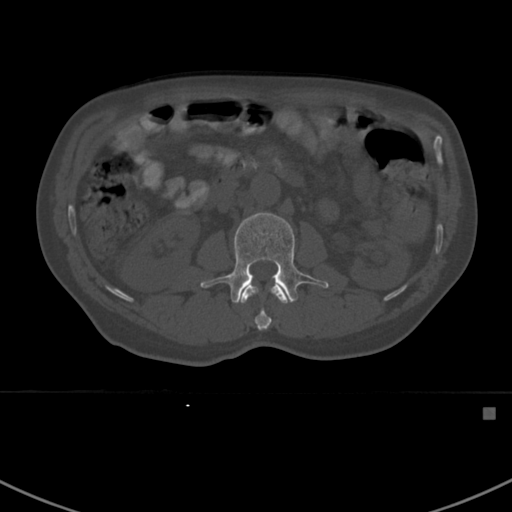
CT including the spine, one axial slice; slice 292 of 412 in the series (ordered by position); reconstruction kernel Br40s; 120 kVp; bone window (W 1800 / L 400 HU); 1.5 mm slice thickness; 512 × 512 image matrix. Patient: male, 59 years. From the clinical record (not read from this slice): primary cancer: prostate.
Structures marked on this image (semi-automatically segmented with operator editing):
- L1 vertebra: bounding box (x1, y1, x2, y2) in pixels: (241, 285, 287, 331)
- L2 vertebra: (200, 212, 329, 303)